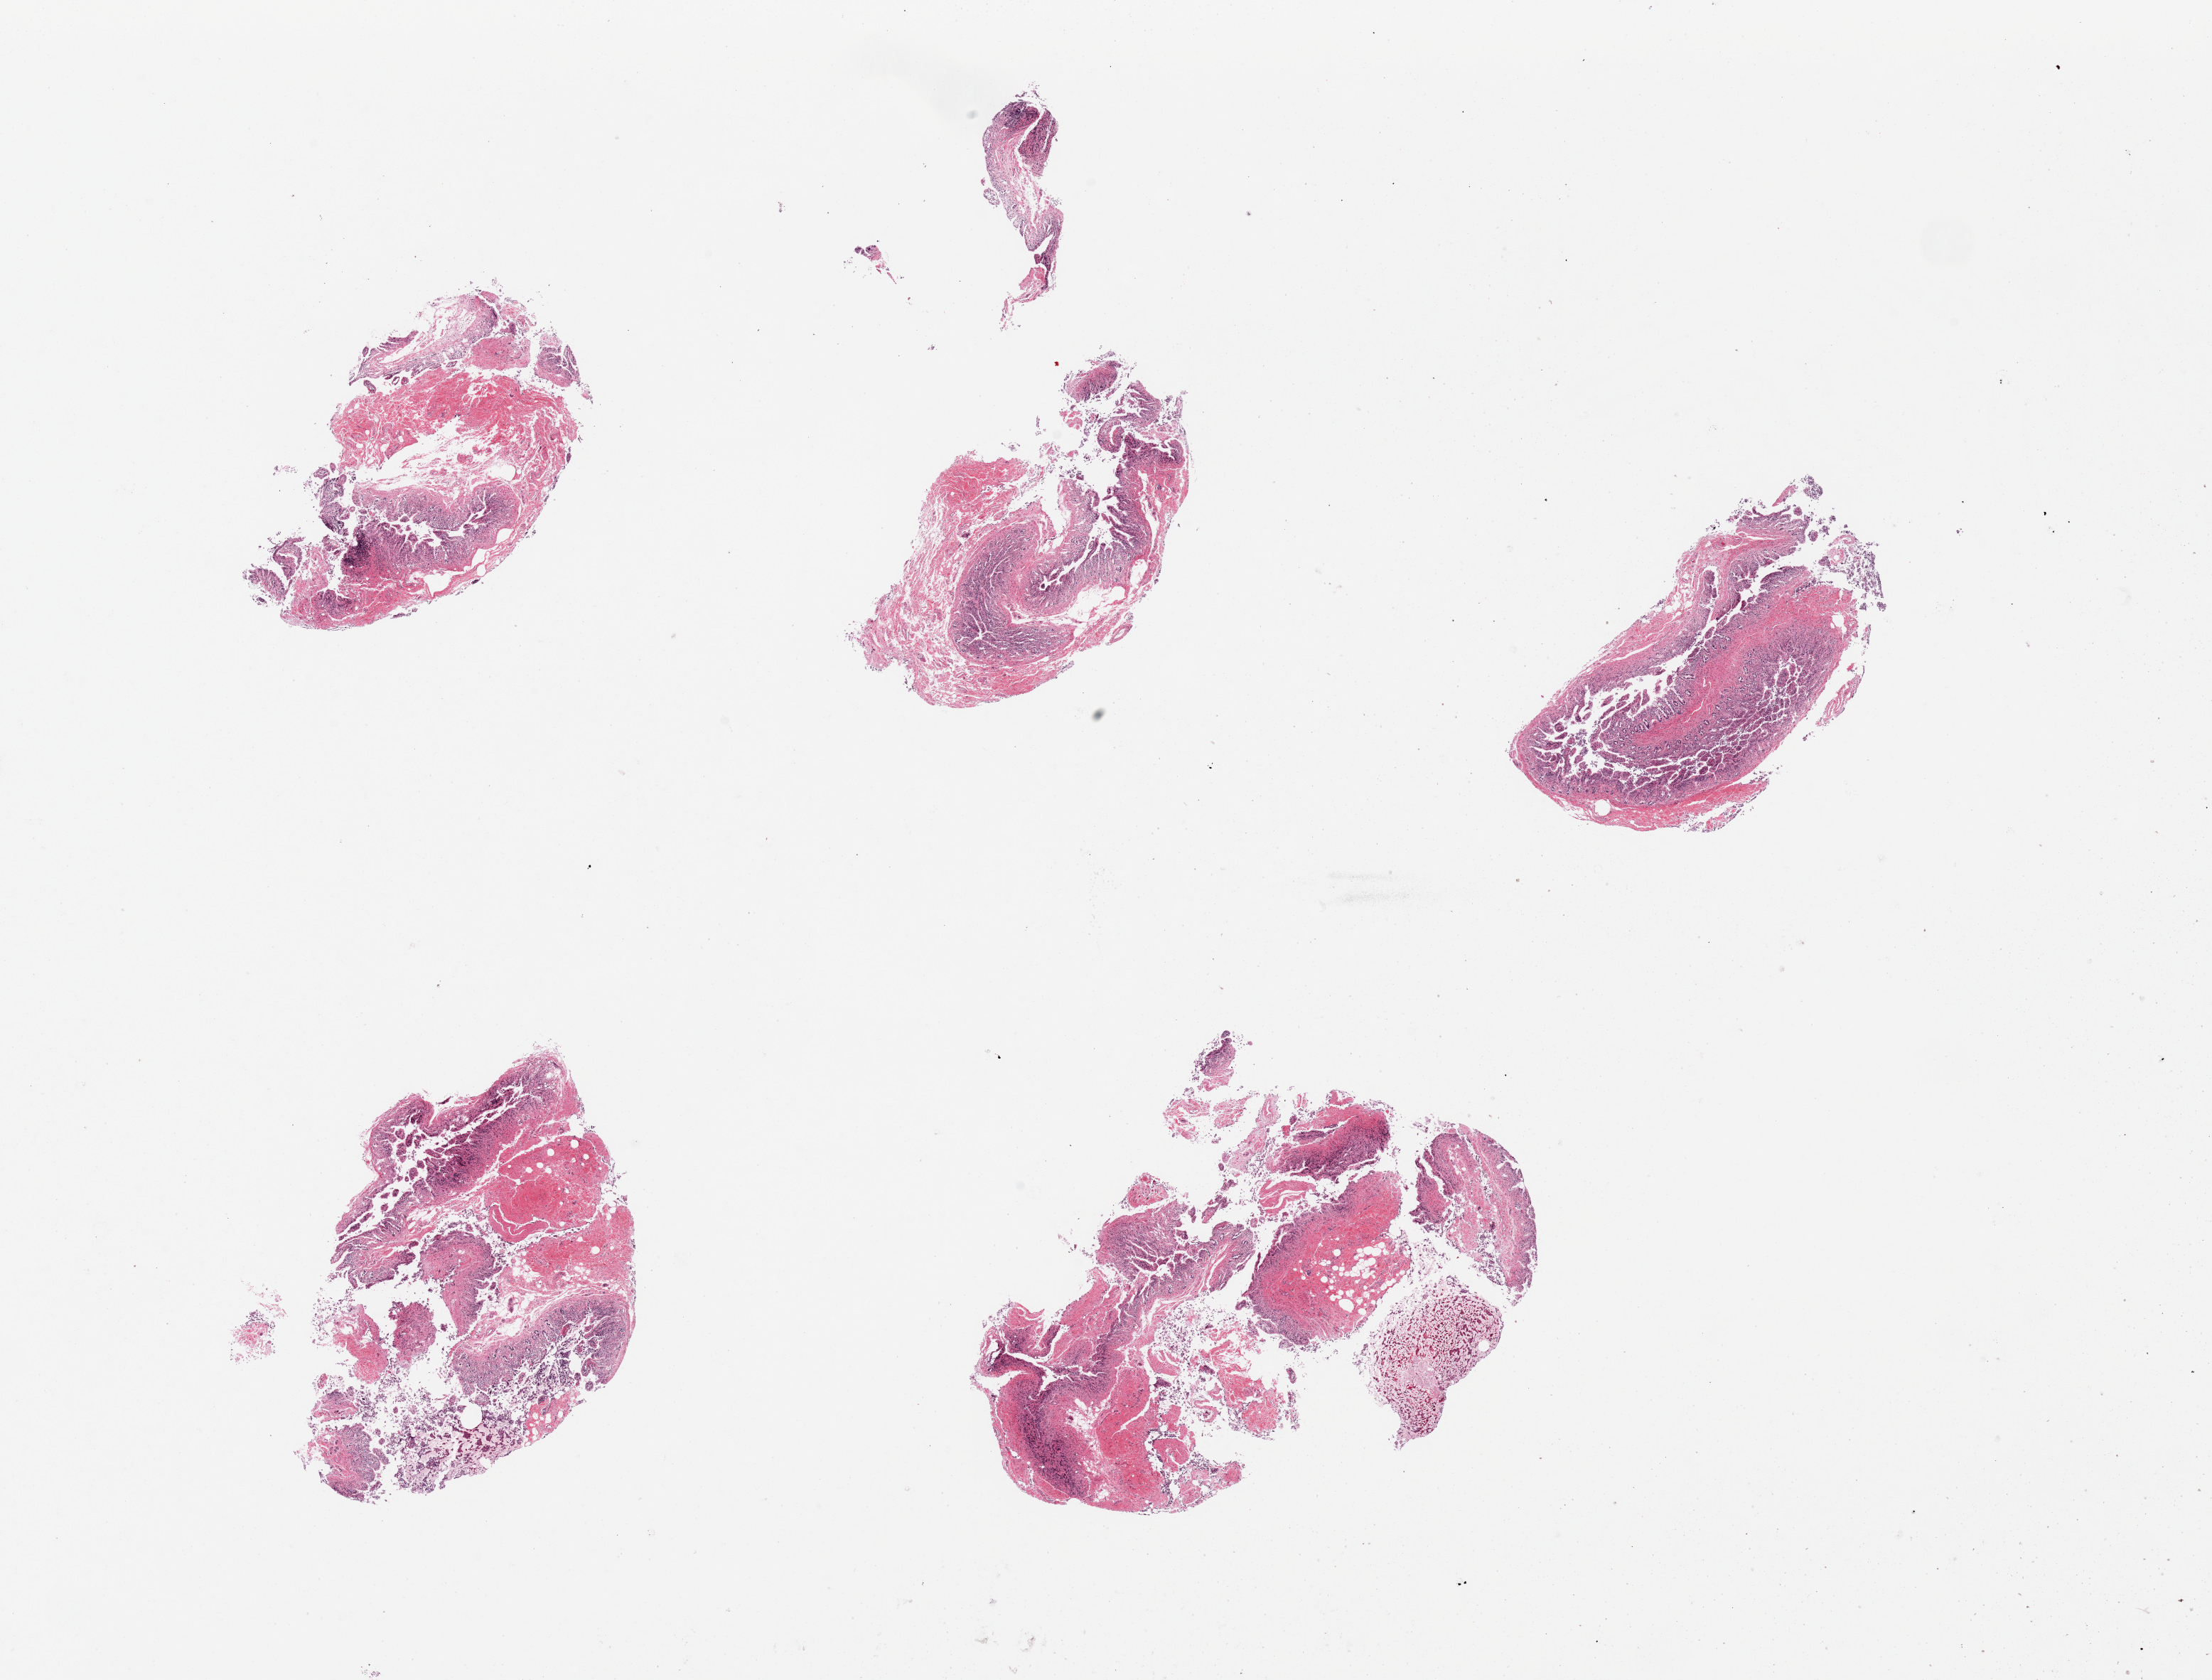
Digitized H&E-stained section, shown as a low-resolution overview of the whole scanned area (about 24.6 x 18.7 mm, slide scanned at 20x), PAXgene-fixed paraffin-embedded (PFPE) section, sampled site (target tissue): ileum, tissue donor sample. Donor: male.
Review note (as recorded): 5 pieces, no lymphoid tissue.